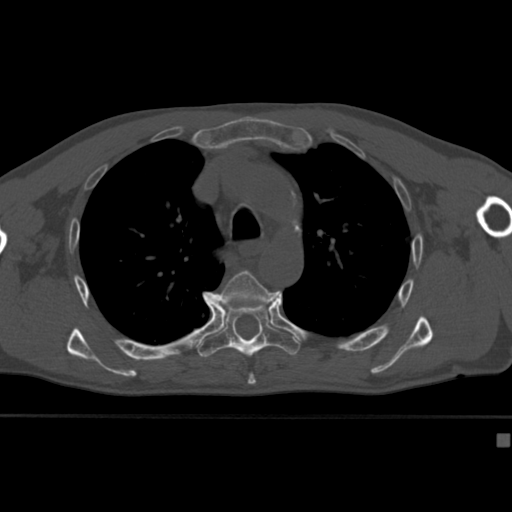
CT including the spine, one axial slice. Position 300 of 430 along the scan axis. Reconstruction kernel Br40s. 120 kVp. Bone window (W 1800 / L 400 HU). 512 × 512 image matrix. Male patient, age 64 years. Case-level facts recorded for this patient, not image findings: primary cancer: uterus; vertebrae with lytic lesions (as recorded): T1, T4, T5, T7, L5.
Outlined on this slice (semi-automatically segmented with operator editing):
- T5 vertebra: box from (x=212, y=270) to (x=281, y=382) px
- T6 vertebra: (x=197, y=303)–(x=301, y=358)